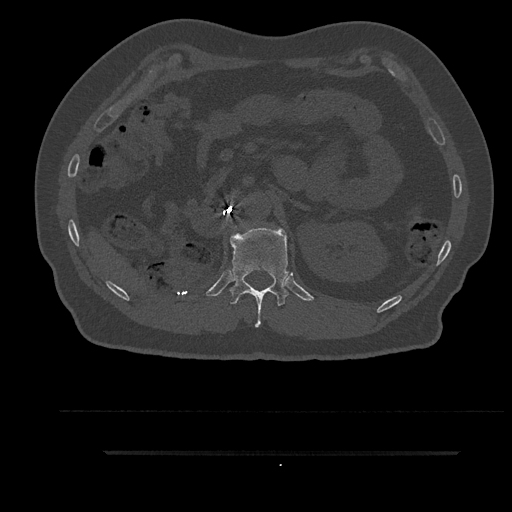
CT including the spine, one axial slice; slice 237 of 797 in the series (ordered by position); bone window (W 1800 / L 400 HU); 0.5 mm slice thickness; 512 × 512 image matrix, field of view 432 × 432 mm. Patient: male, 63 years. From the clinical record (not read from this slice): primary cancer: renal; vertebrae with lytic lesions (as recorded): T8.
Outlined on this slice (semi-automatic segmentation, software-assisted and operator-edited):
- T12 vertebra: bounding box <229,227,288,328> (left, top, right, bottom; pixels)